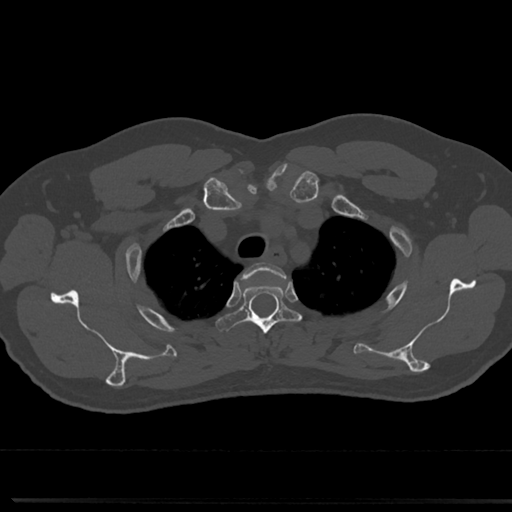
CT including the spine, one axial slice. Position 600 of 817 along the scan axis. 120 kVp. Bone window (W 1800 / L 400 HU). 0.5 mm slice thickness. 512 × 512 image matrix, field of view 355 × 355 mm. Male patient, age 61 years. Case-level facts recorded for this patient, not image findings: primary cancer: prostate.
Structures marked on this image (semi-automatically segmented with operator editing):
- T2 vertebra: bounding box [x1, y1, x2, y2] px = [247, 263, 282, 276]
- T3 vertebra: [221, 275, 296, 341]